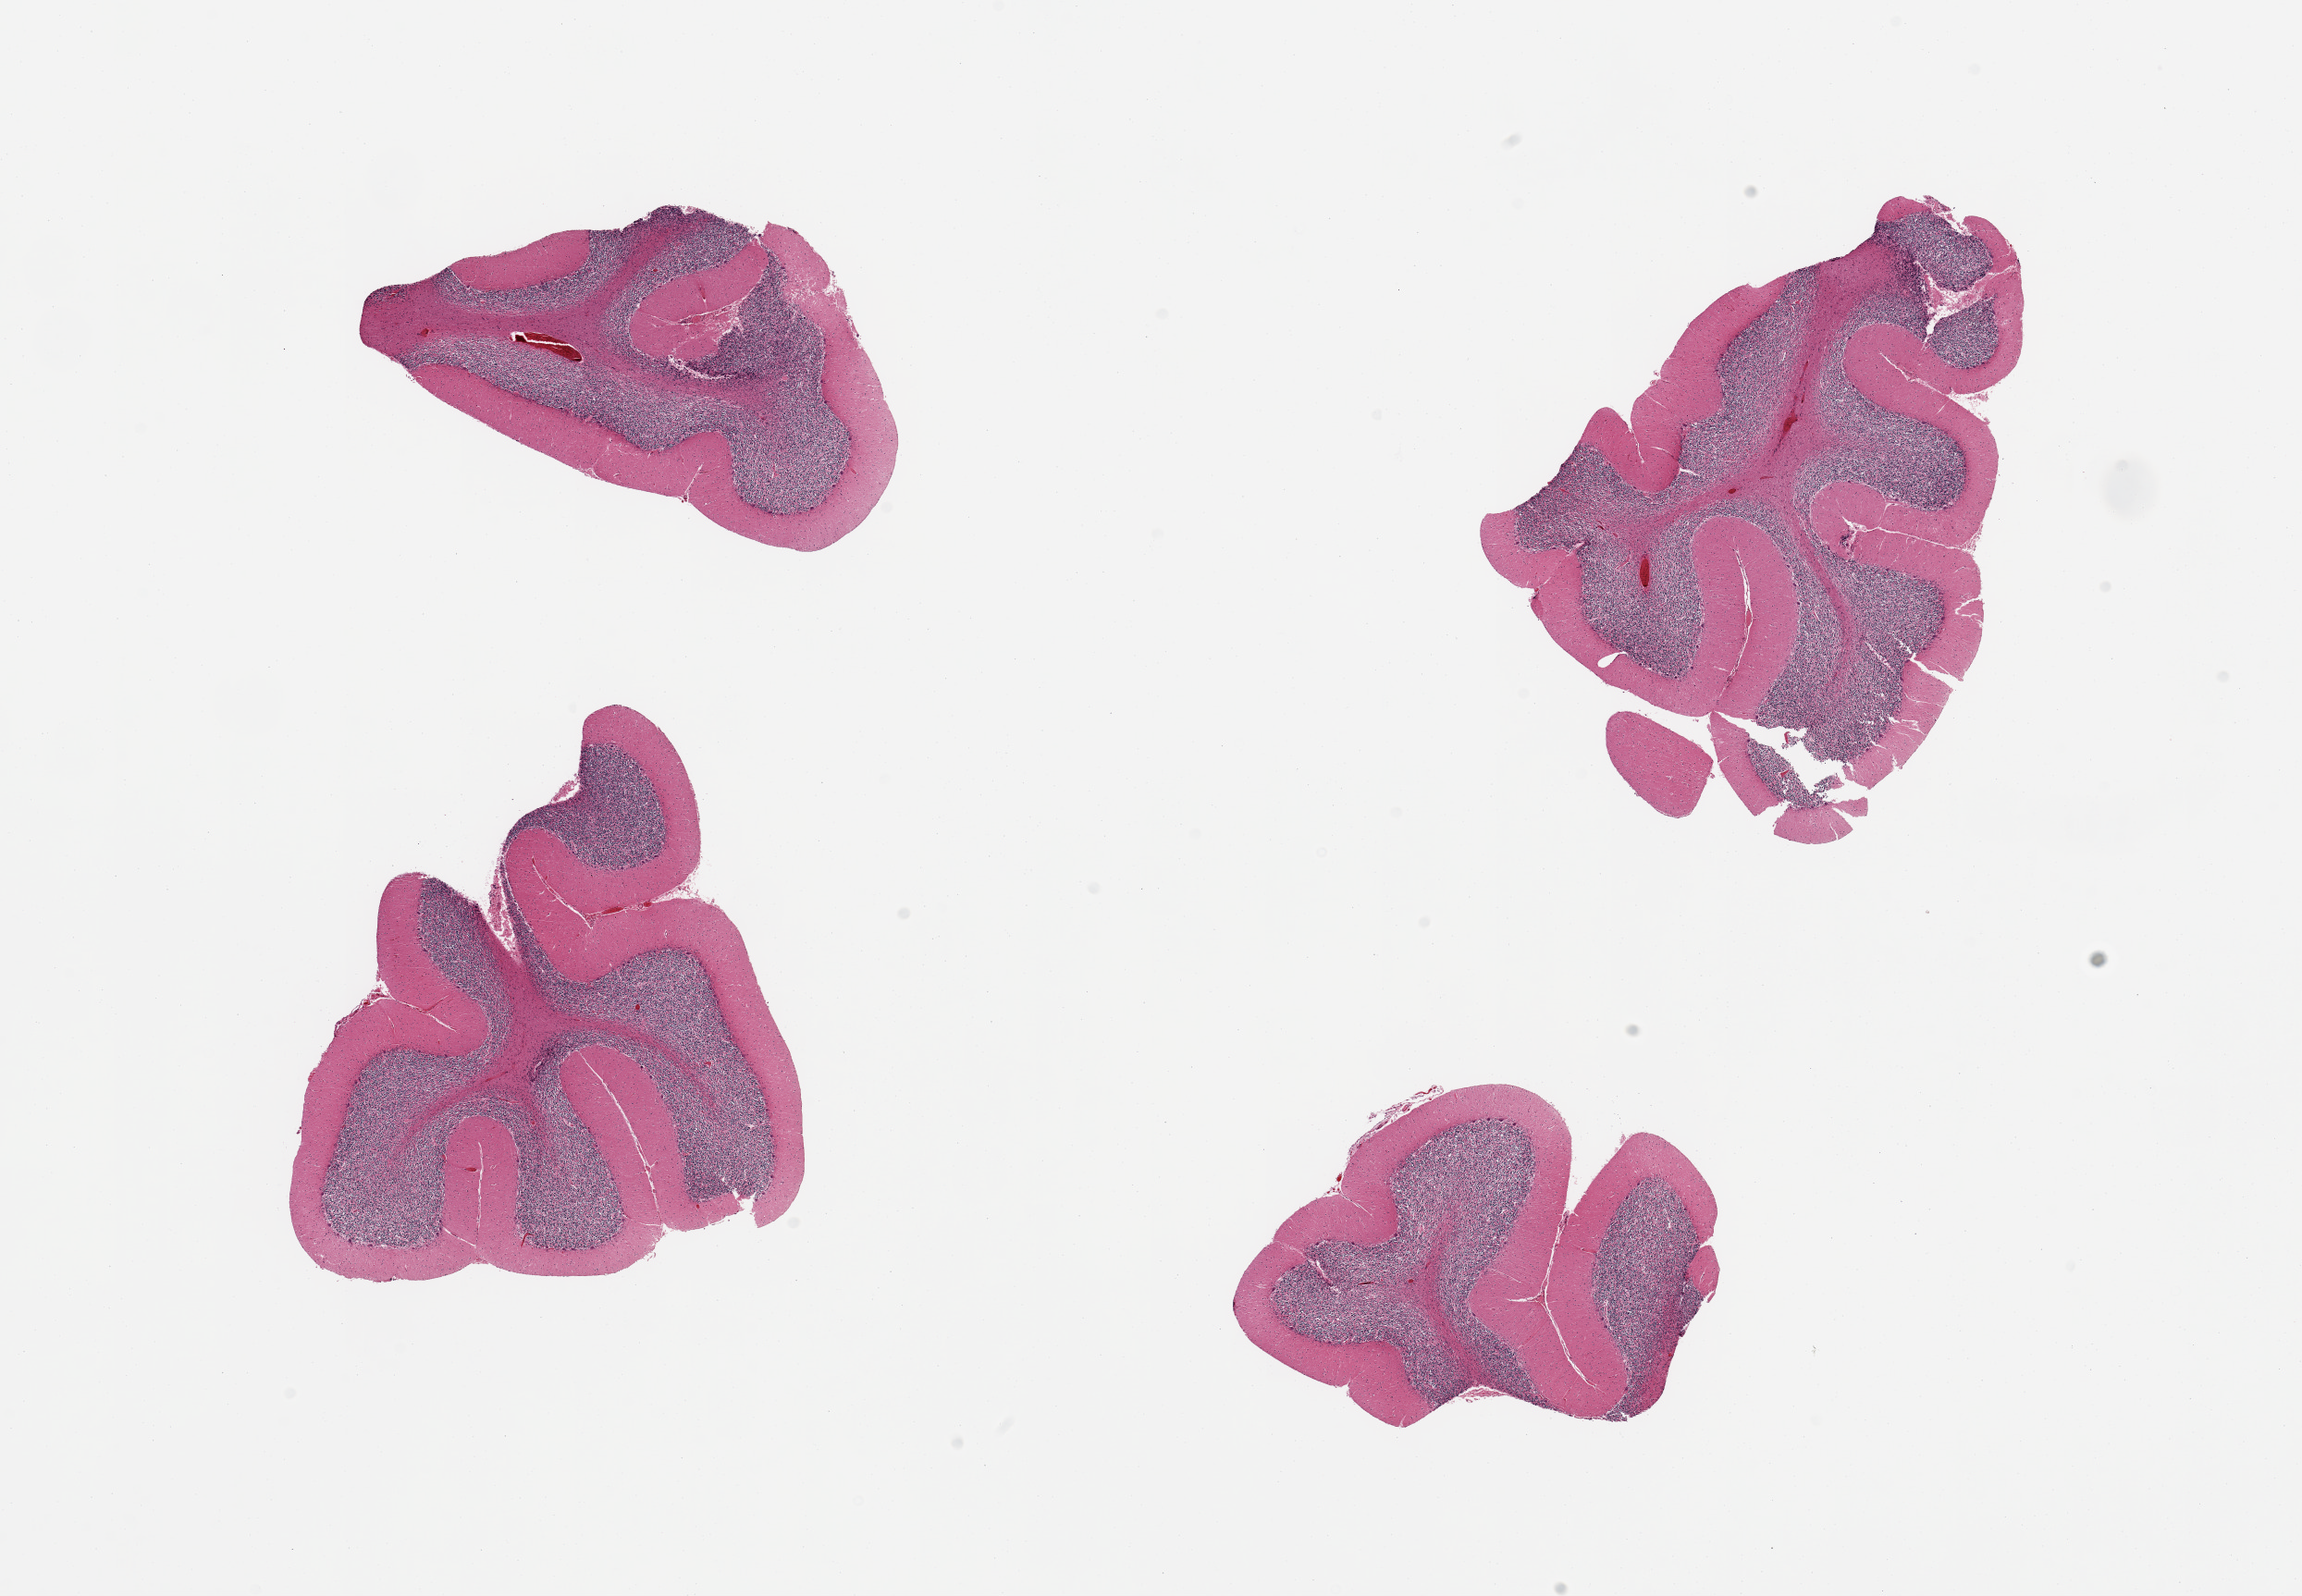
Haematoxylin and eosin whole-slide image, a low-resolution overview of the entire scanned area, about 19.7 x 13.7 mm. PAXgene-fixed, paraffin-embedded tissue. Section of cerebellum (target tissue). Tissue donor sample.
* reviewer comment on this tissue sample: 4 pieces